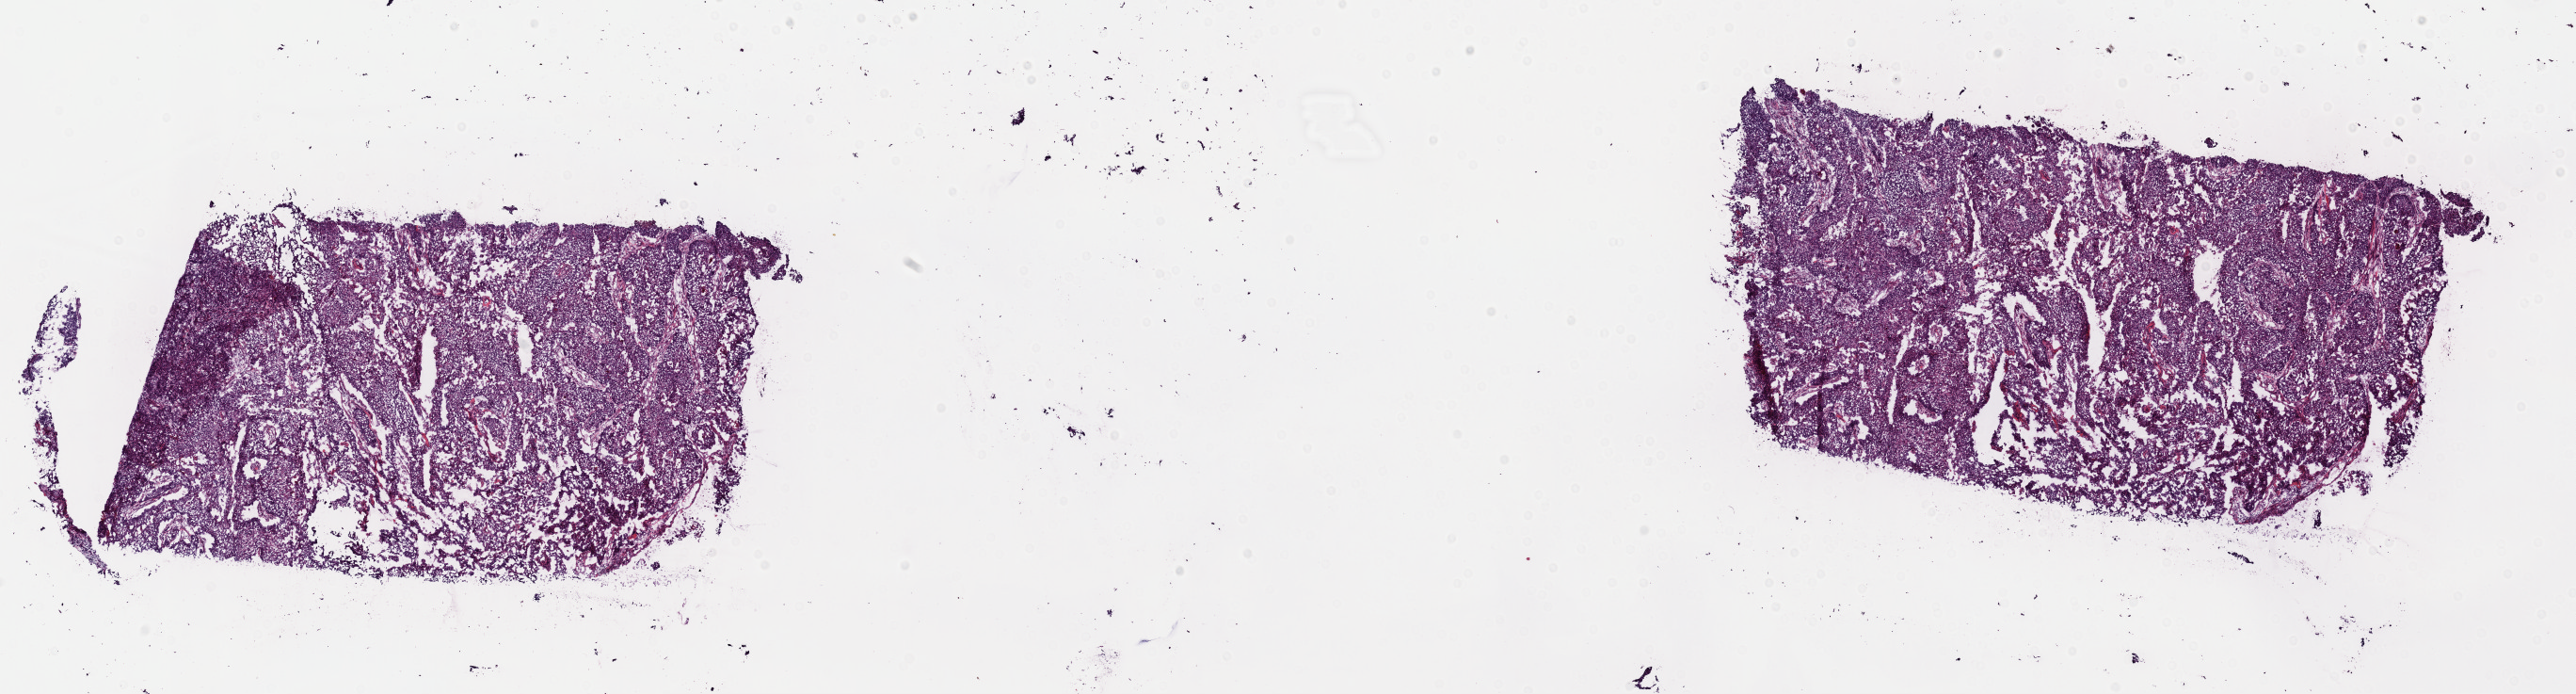
Hematoxylin and eosin (H&E) stained whole-slide image, shown as a low-resolution overview of the whole scanned area (about 21.6 x 5.8 mm, slide scanned at 40x), frozen section from the top of the tissue portion, uterus, primary tumour sample. Patient: female, age at initial diagnosis 63 years. Histologic grade: G3 (poorly differentiated). Pathologist review of this section (percent, as recorded): tumour cells 60%, tumour nuclei 60%, normal cells 0%, stromal cells 30%, necrosis 10%. Infiltration values recorded for this section: lymphocyte infiltration 40%, monocyte infiltration 20%, neutrophil infiltration 20%.
Pathologic diagnosis: Endometrioid adenocarcinoma, NOS (endometrium). FIGO stage: IIIB.